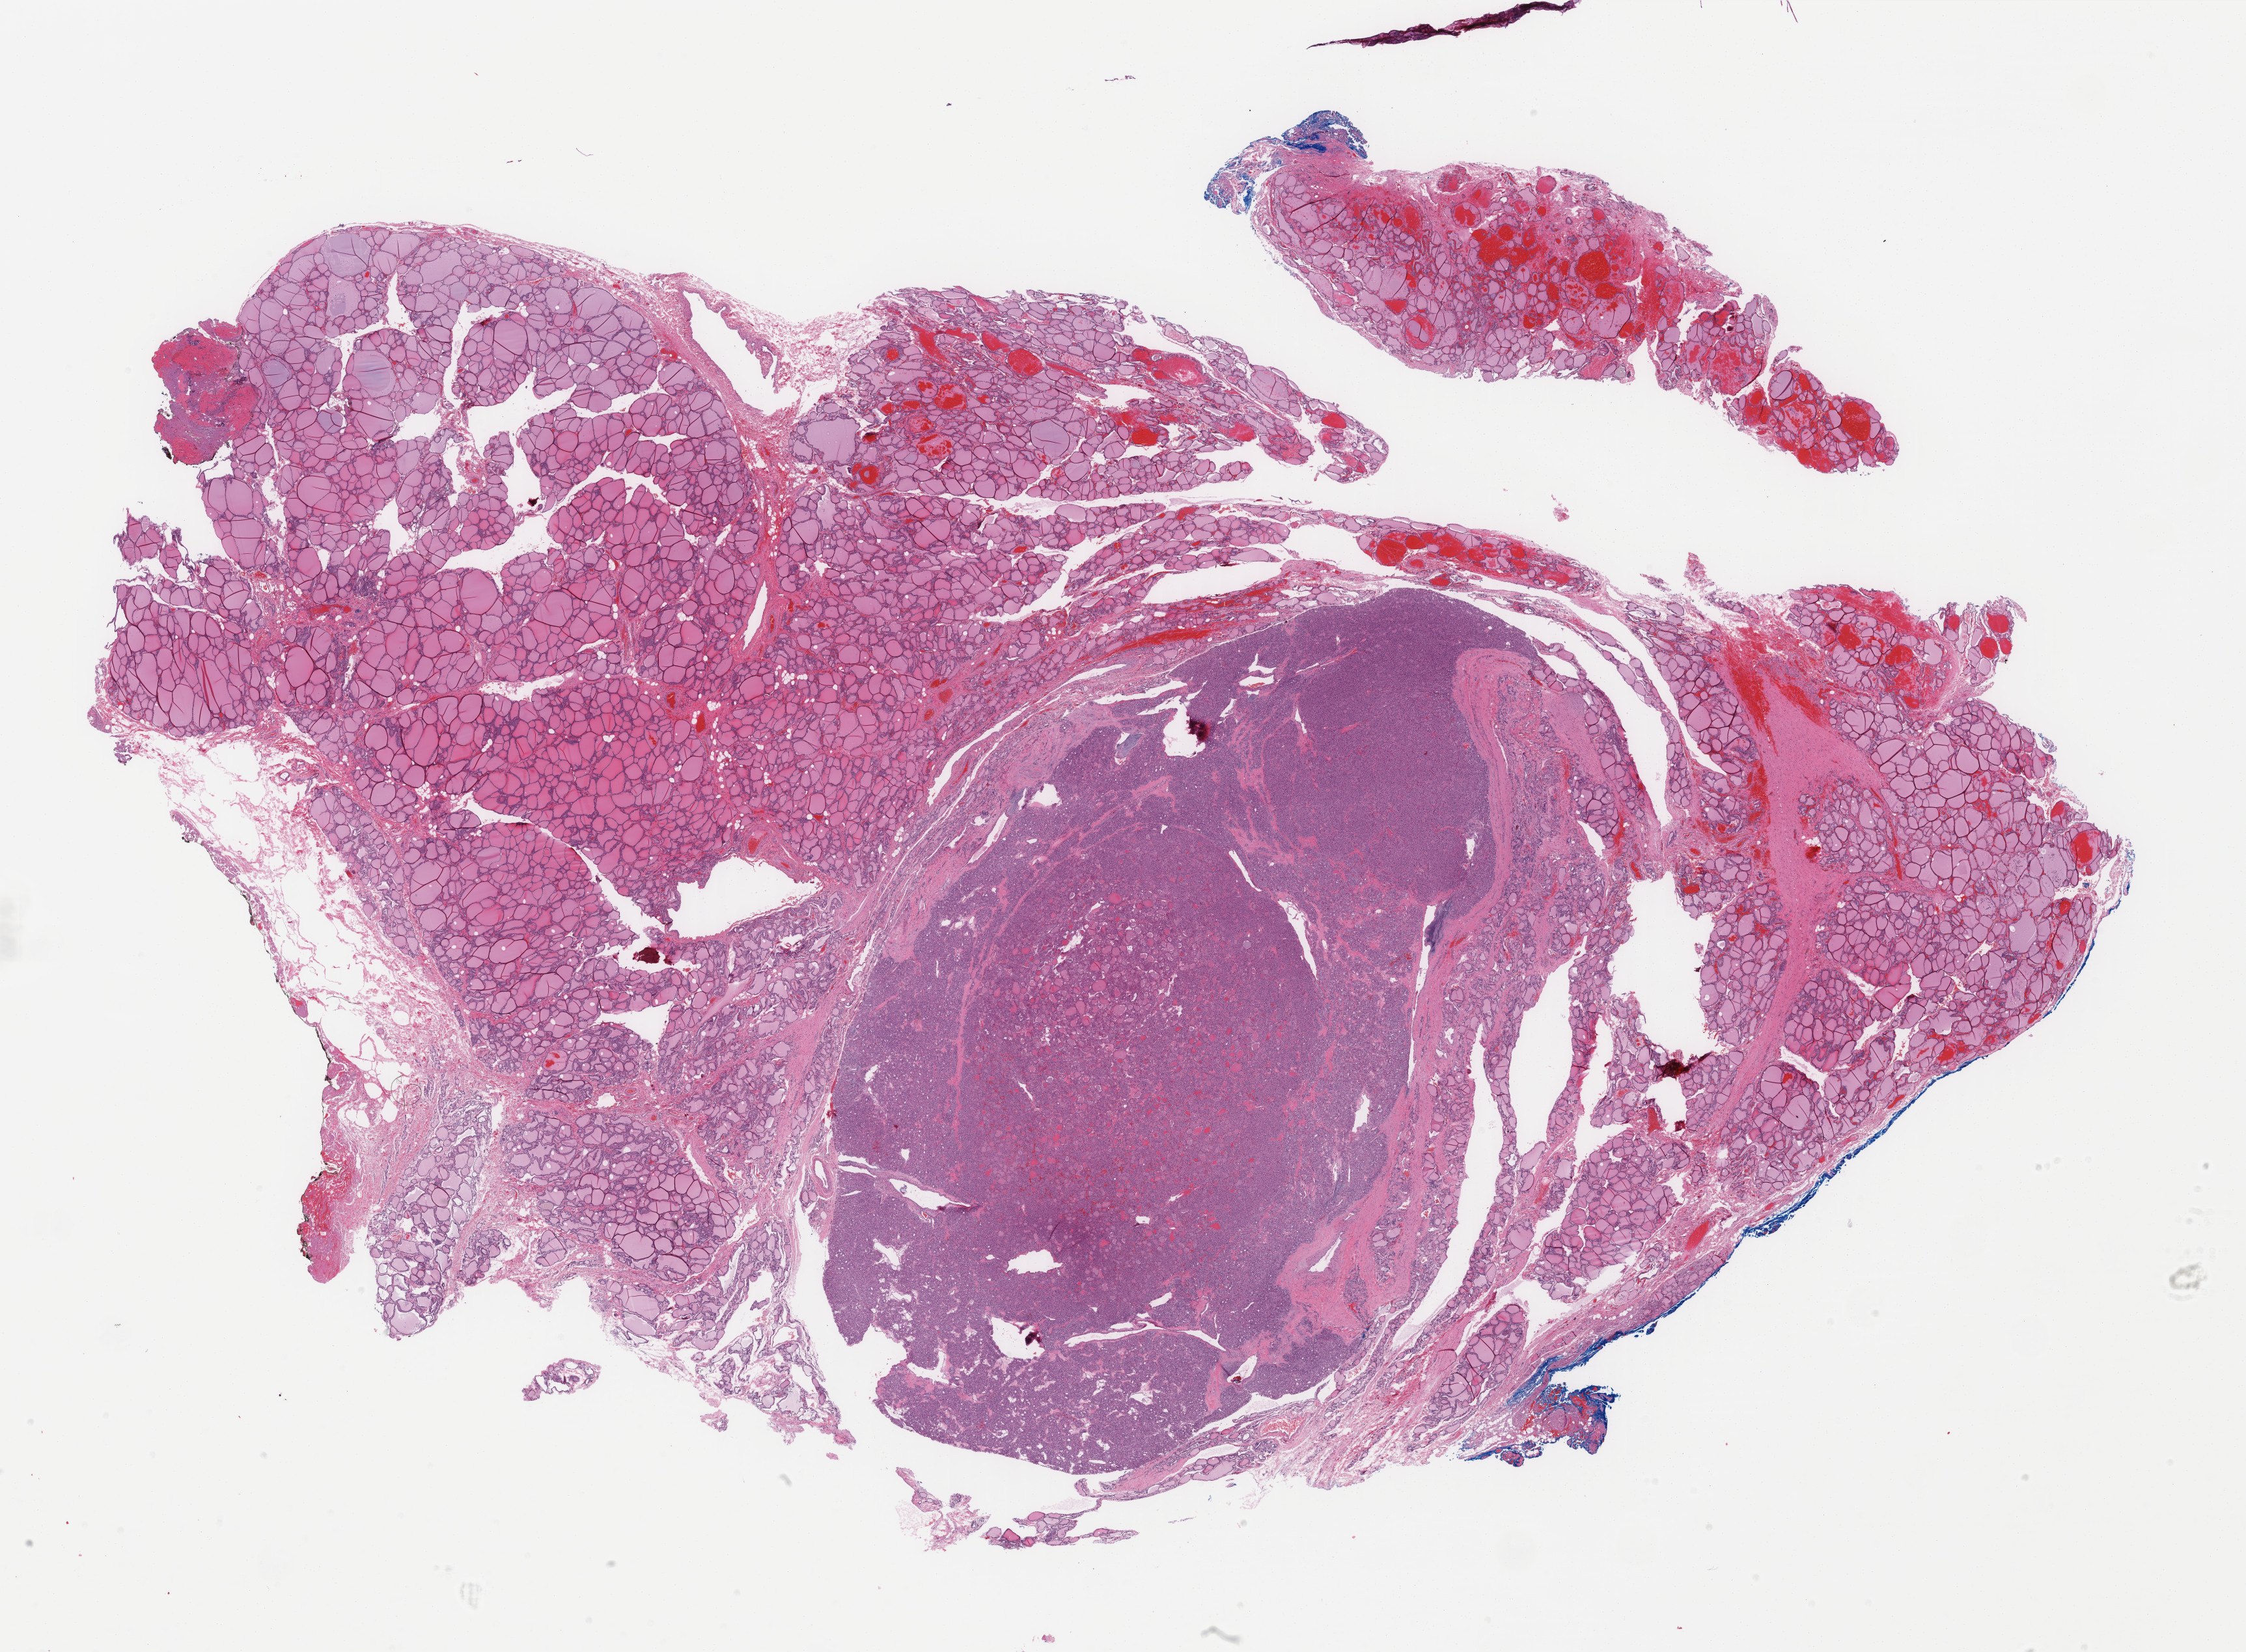
Digitized H&E-stained tissue section (whole slide) — shown as a low-resolution overview of the whole scanned area (about 27.4 x 20.1 mm, slide scanned at 40x); FFPE section; thyroid, primary tumour sample. Female, age 19 years at initial diagnosis.
- histologic diagnosis: Papillary carcinoma, follicular variant (thyroid gland)
- AJCC pathologic stage: I